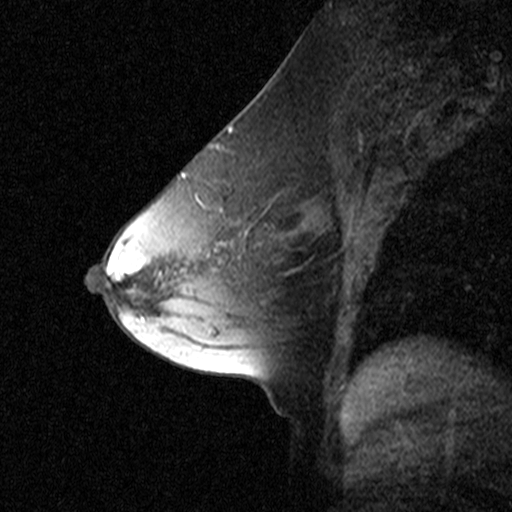
Breast MRI (dynamic contrast-enhanced), one sagittal slice. Position 26 of 44 along the scan axis. Dynamic contrast-enhanced study with each time point stored as its own series, time point 2 of 3 at this slice position (early post-contrast, ordered by acquisition time). 1.5 T. TE 4.5 ms, TR 11 ms. 512 × 512 image matrix, field of view 200 × 200 mm. Patient: female, 53 years. From the clinical record (not read from this slice): setting: breast cancer imaged before/during neoadjuvant chemotherapy; receptor status: HR-positive, HER2-negative.
Outlined on this slice (semi-automatic segmentation, software-assisted and operator-edited):
- analysis volume of interest (the breast-tissue region the enhancement analysis was run in; not a lesion): bounding box <170,150,277,273> (left, top, right, bottom; pixels)
- tumour enhancement mask (voxels above the 90 % enhancement threshold inside the analysis volume of interest): <181,173,188,176>